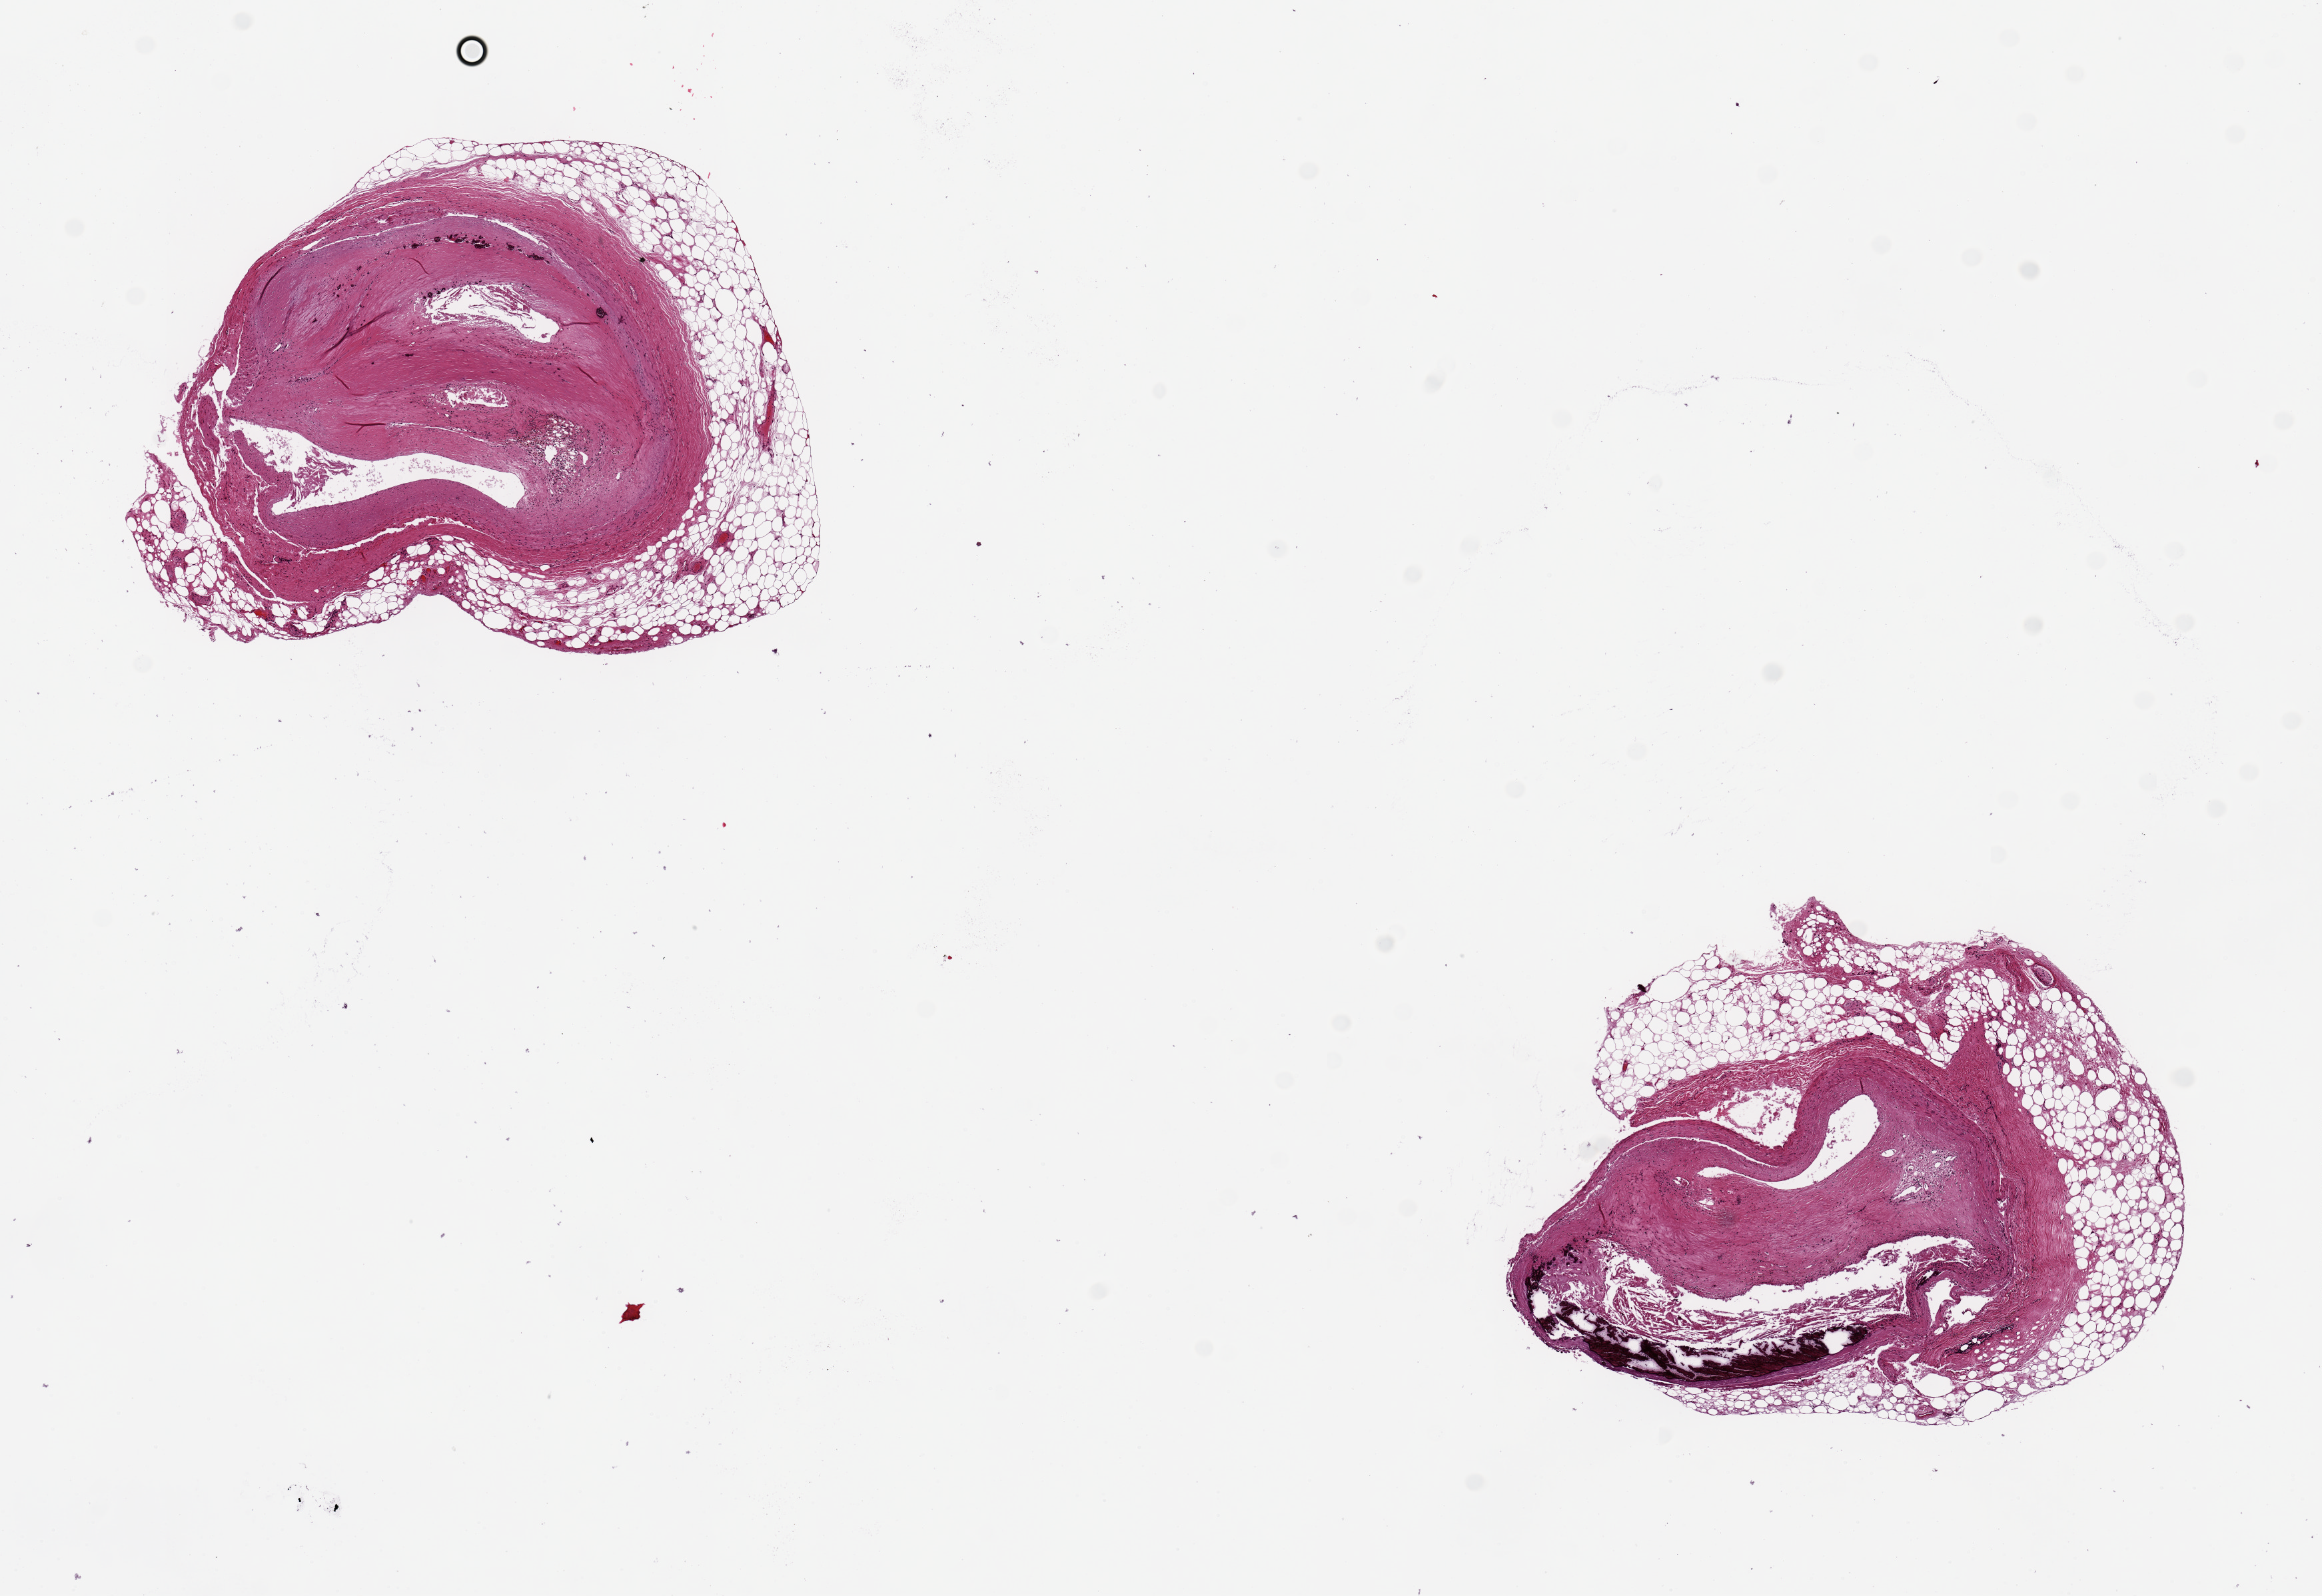
Digitized hematoxylin and eosin (H&E)-stained section — whole scanned area (about 13.8 x 9.5 mm) shown as a low-resolution overview, PAXgene-fixed paraffin-embedded (PFPE) section, section of coronary artery (target tissue), tissue donor sample. Female donor.
Reviewer comment on this tissue sample: 2 pieces, 4x2 & 4x3.5mm; ~3mm arteries with extensive atherosclerosis and old and recent intramural hemorrhages narrowing lumen to about 10%; adipose encases arteries up to ~0.8mm.